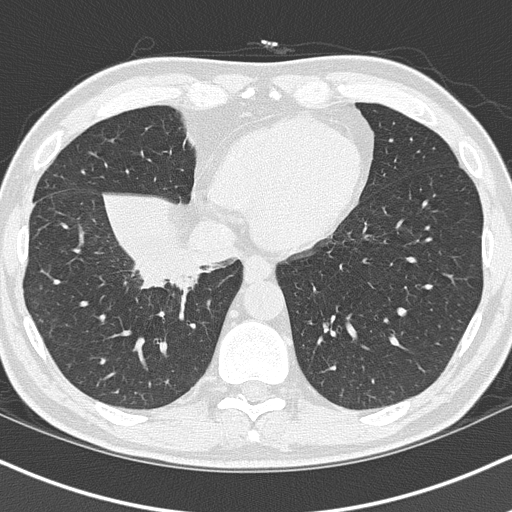
Low-dose screening chest CT, one axial slice. Slice 35 of 151 in the series (ordered by position). Reconstruction kernel B50f. 120 kVp. Lung window (W 1500 / L -600 HU). 2 mm slice thickness. 512 × 512 image matrix, field of view 320 × 320 mm.
Outlined on this slice (manually delineated by an expert):
- lesion 1 (tumor, hilum of right lung): box from (x=126, y=231) to (x=201, y=285) px